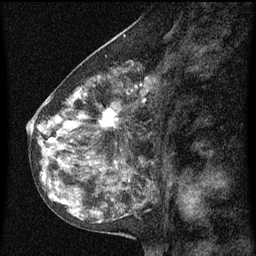
Breast MRI (dynamic contrast-enhanced), one sagittal slice. Slice 35 of 60 in the series (ordered by position). Dynamic contrast-enhanced series, image 2 of 3 at this slice position (ordered by acquisition). 1.5 T. TE 4.2 ms, TR 8 ms. 256 × 256 image matrix. Patient: female, 55 years.
Annotated regions visible in this slice (semi-automatically segmented with operator editing):
- analysis volume of interest (the breast-tissue region the enhancement analysis was run in; not a lesion): bounding box [x1, y1, x2, y2] px = [34, 68, 155, 151]
- tumour enhancement mask (voxels above the 70 % enhancement threshold inside the analysis volume of interest): [38, 72, 149, 151]